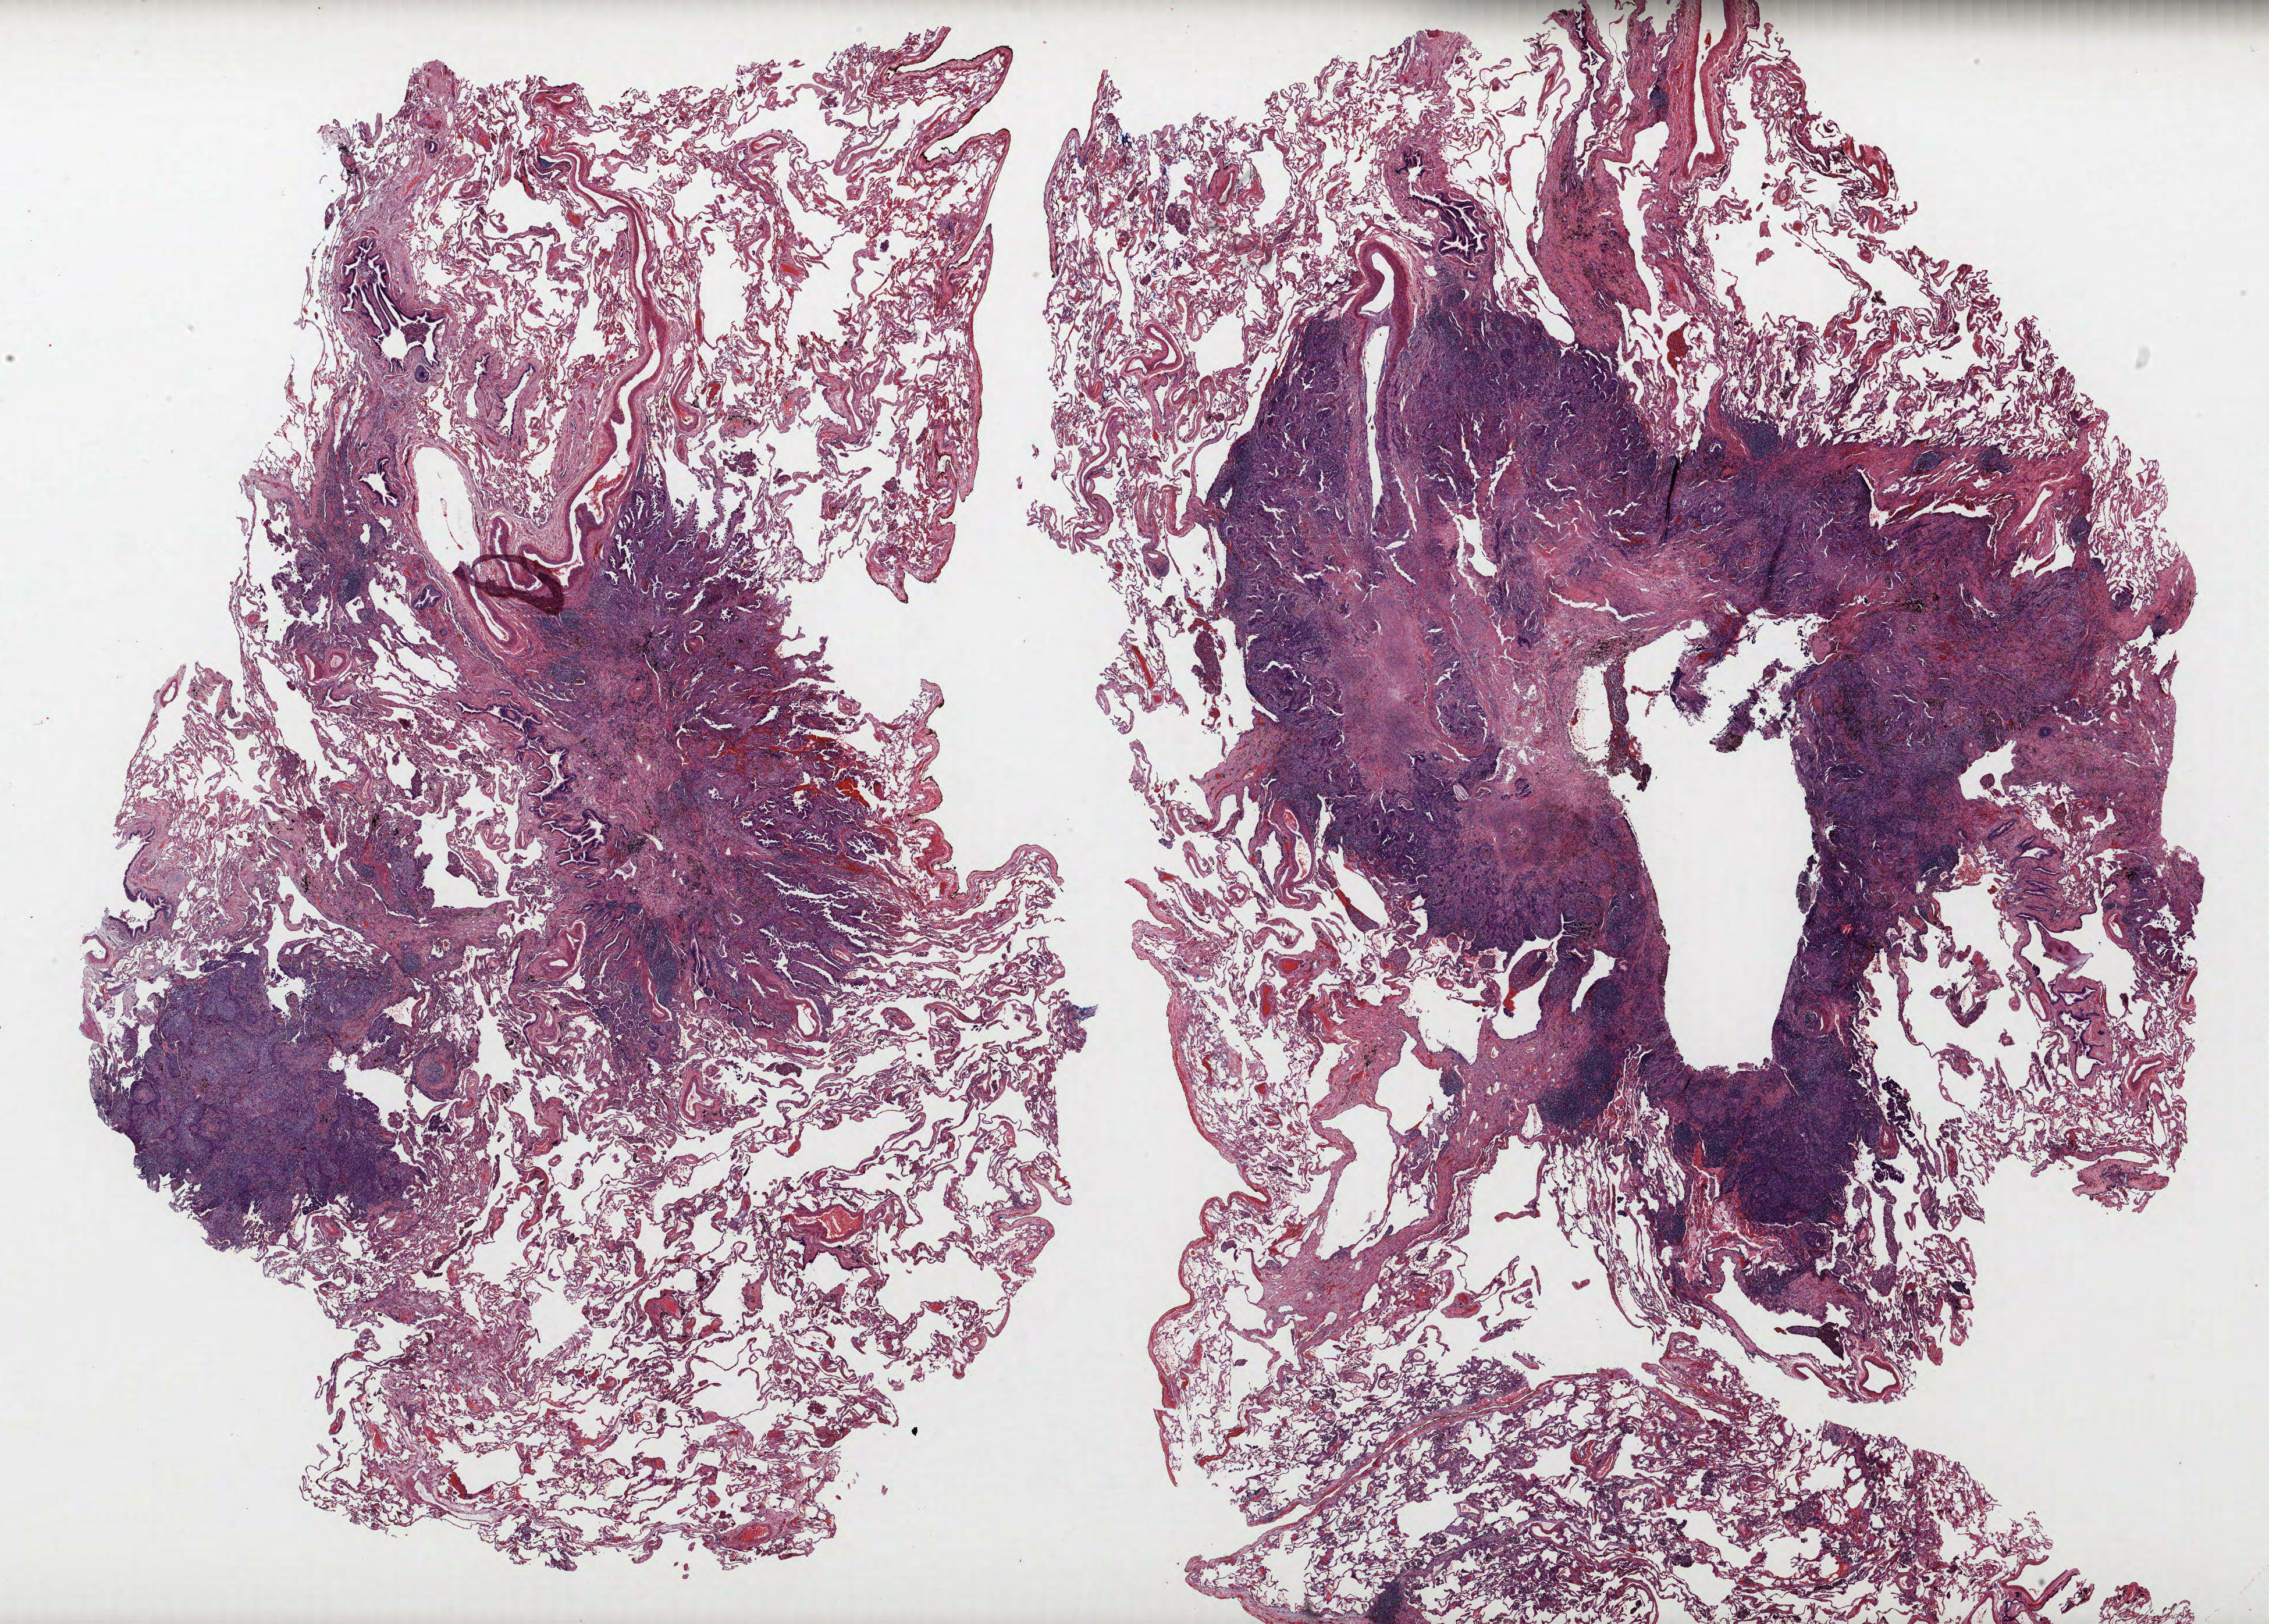
Whole-slide histology image, Hematoxylin and eosin (H&E) stained, shown as a low-resolution overview of the whole scanned area (about 31.2 x 22.3 mm, from a 40x scan), formalin-fixed paraffin-embedded (FFPE) section, lung tissue. Female patient, aged 64 at enrolment. Current smoker at enrolment. Grade: poorly differentiated (G3).
Primary tumour location (clinical record): left upper lobe. Stage (AJCC 6th edition): IA. Tumour size (pathology): 12 mm. Participant's lung-cancer diagnosis: Adenocarcinoma, NOS. ICD-O-3 topography: upper lobe of lung (C34.1).